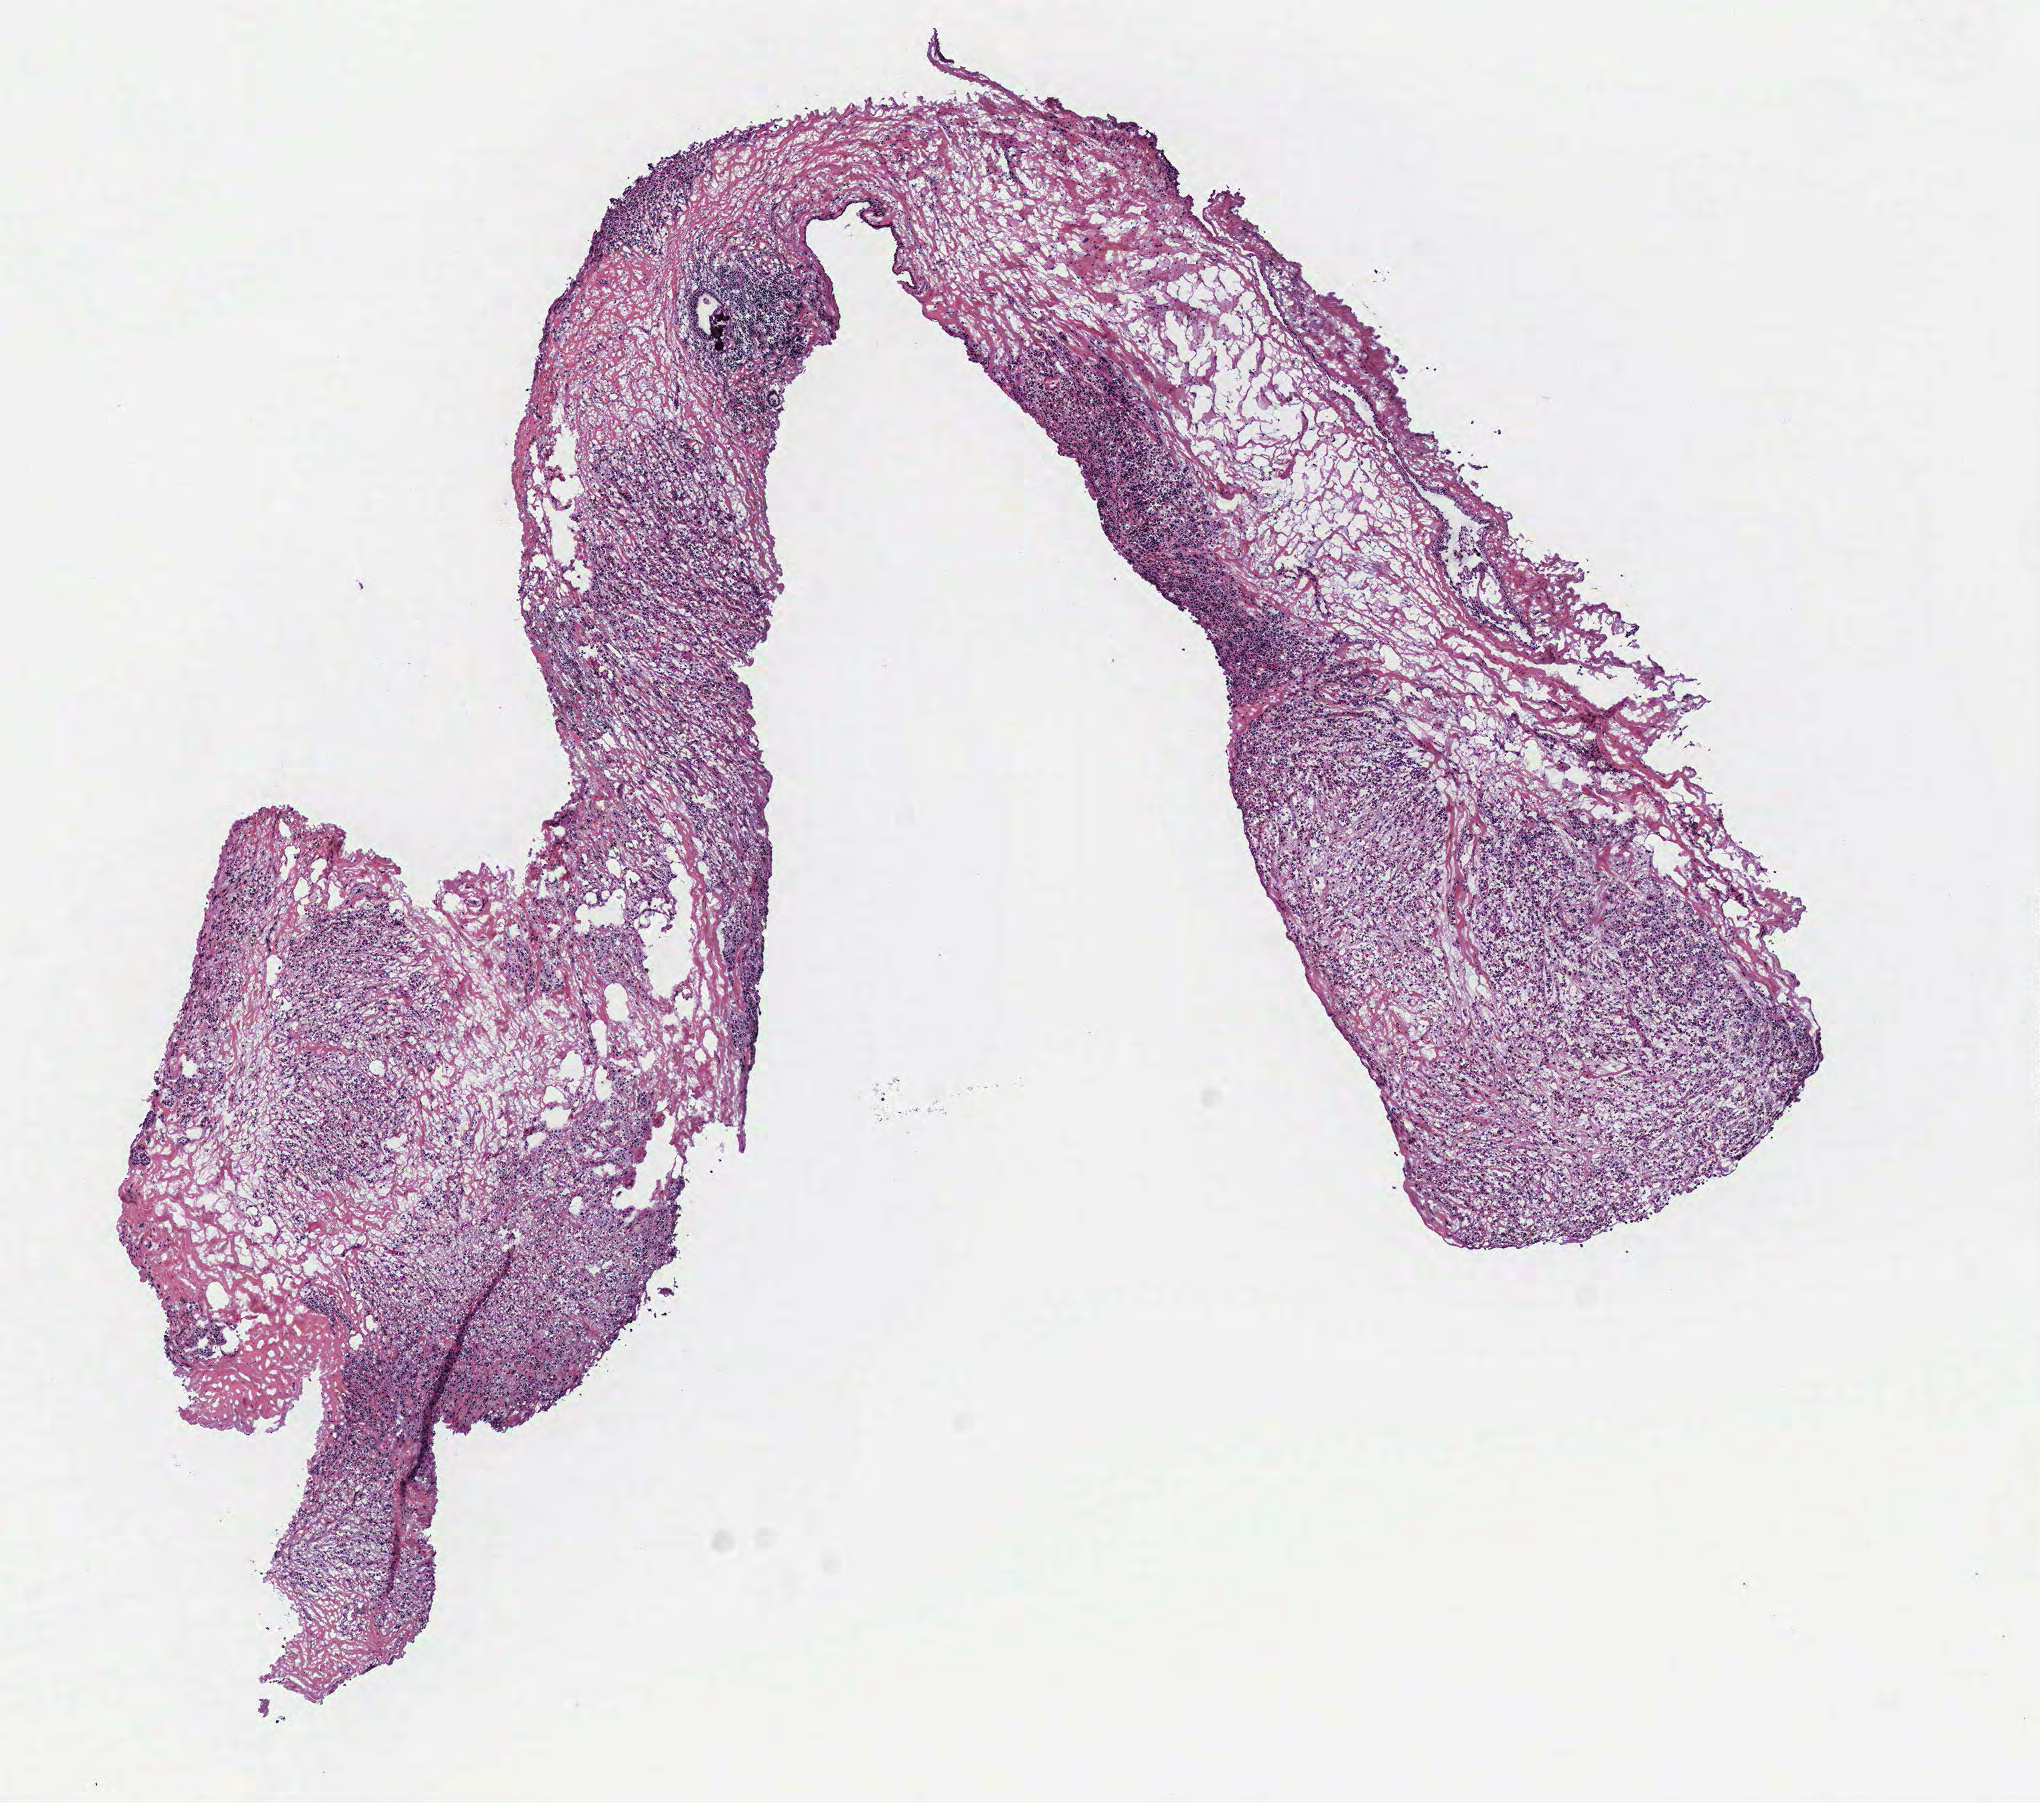
Whole-slide histology image, H&E — shown as a low-resolution overview of the whole scanned area (about 8.2 x 7.2 mm, slide scanned at 40x), tumour tissue sample, breast. Female, 78 y/o.
Histologic diagnosis: Infiltrating lobular carcinoma, NOS. AJCC pathologic stage: IIA.